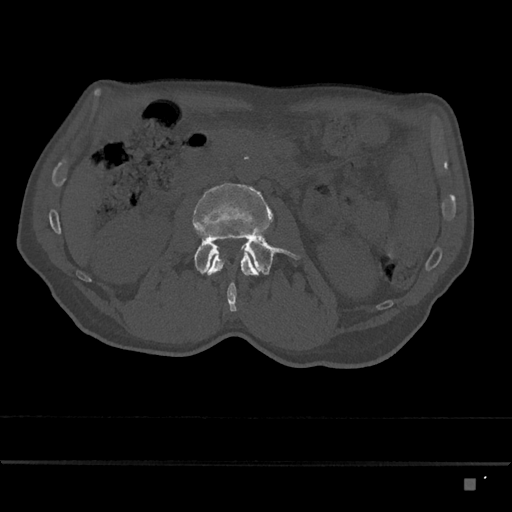
CT including the spine, one axial slice. Position 433 of 797 along the scan axis. Reconstruction kernel Br40s/3. 120 kVp. Bone window (W 1800 / L 400 HU). 512 × 512 image matrix. Male patient, age 72 years. From the clinical record (not read from this slice): primary cancer: prostate.
Structures marked on this image (semi-automatically segmented with operator editing):
- L2 vertebra: bounding box <204,252,259,312> (left, top, right, bottom; pixels)
- L3 vertebra: <192,183,301,275>